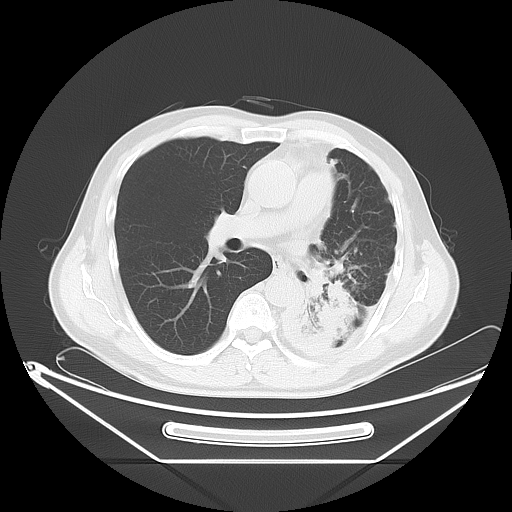
Chest CT, one axial slice; slice 35 of 63 in the series (ordered by position); reconstruction kernel LUNG; 120 kVp; lung window (W 1500 / L -600 HU); 5 mm slice thickness; 512 × 512 image matrix, field of view 442 × 442 mm. Patient: male, 60 years. Case-level facts recorded for this patient, not image findings: clinical TNM (as recorded): T4 N1 M1.
Annotated regions visible in this slice (rectangle marked by the reading radiologist):
- lung tumour (recorded histology: adenocarcinoma): box from (x=292, y=268) to (x=361, y=354) px